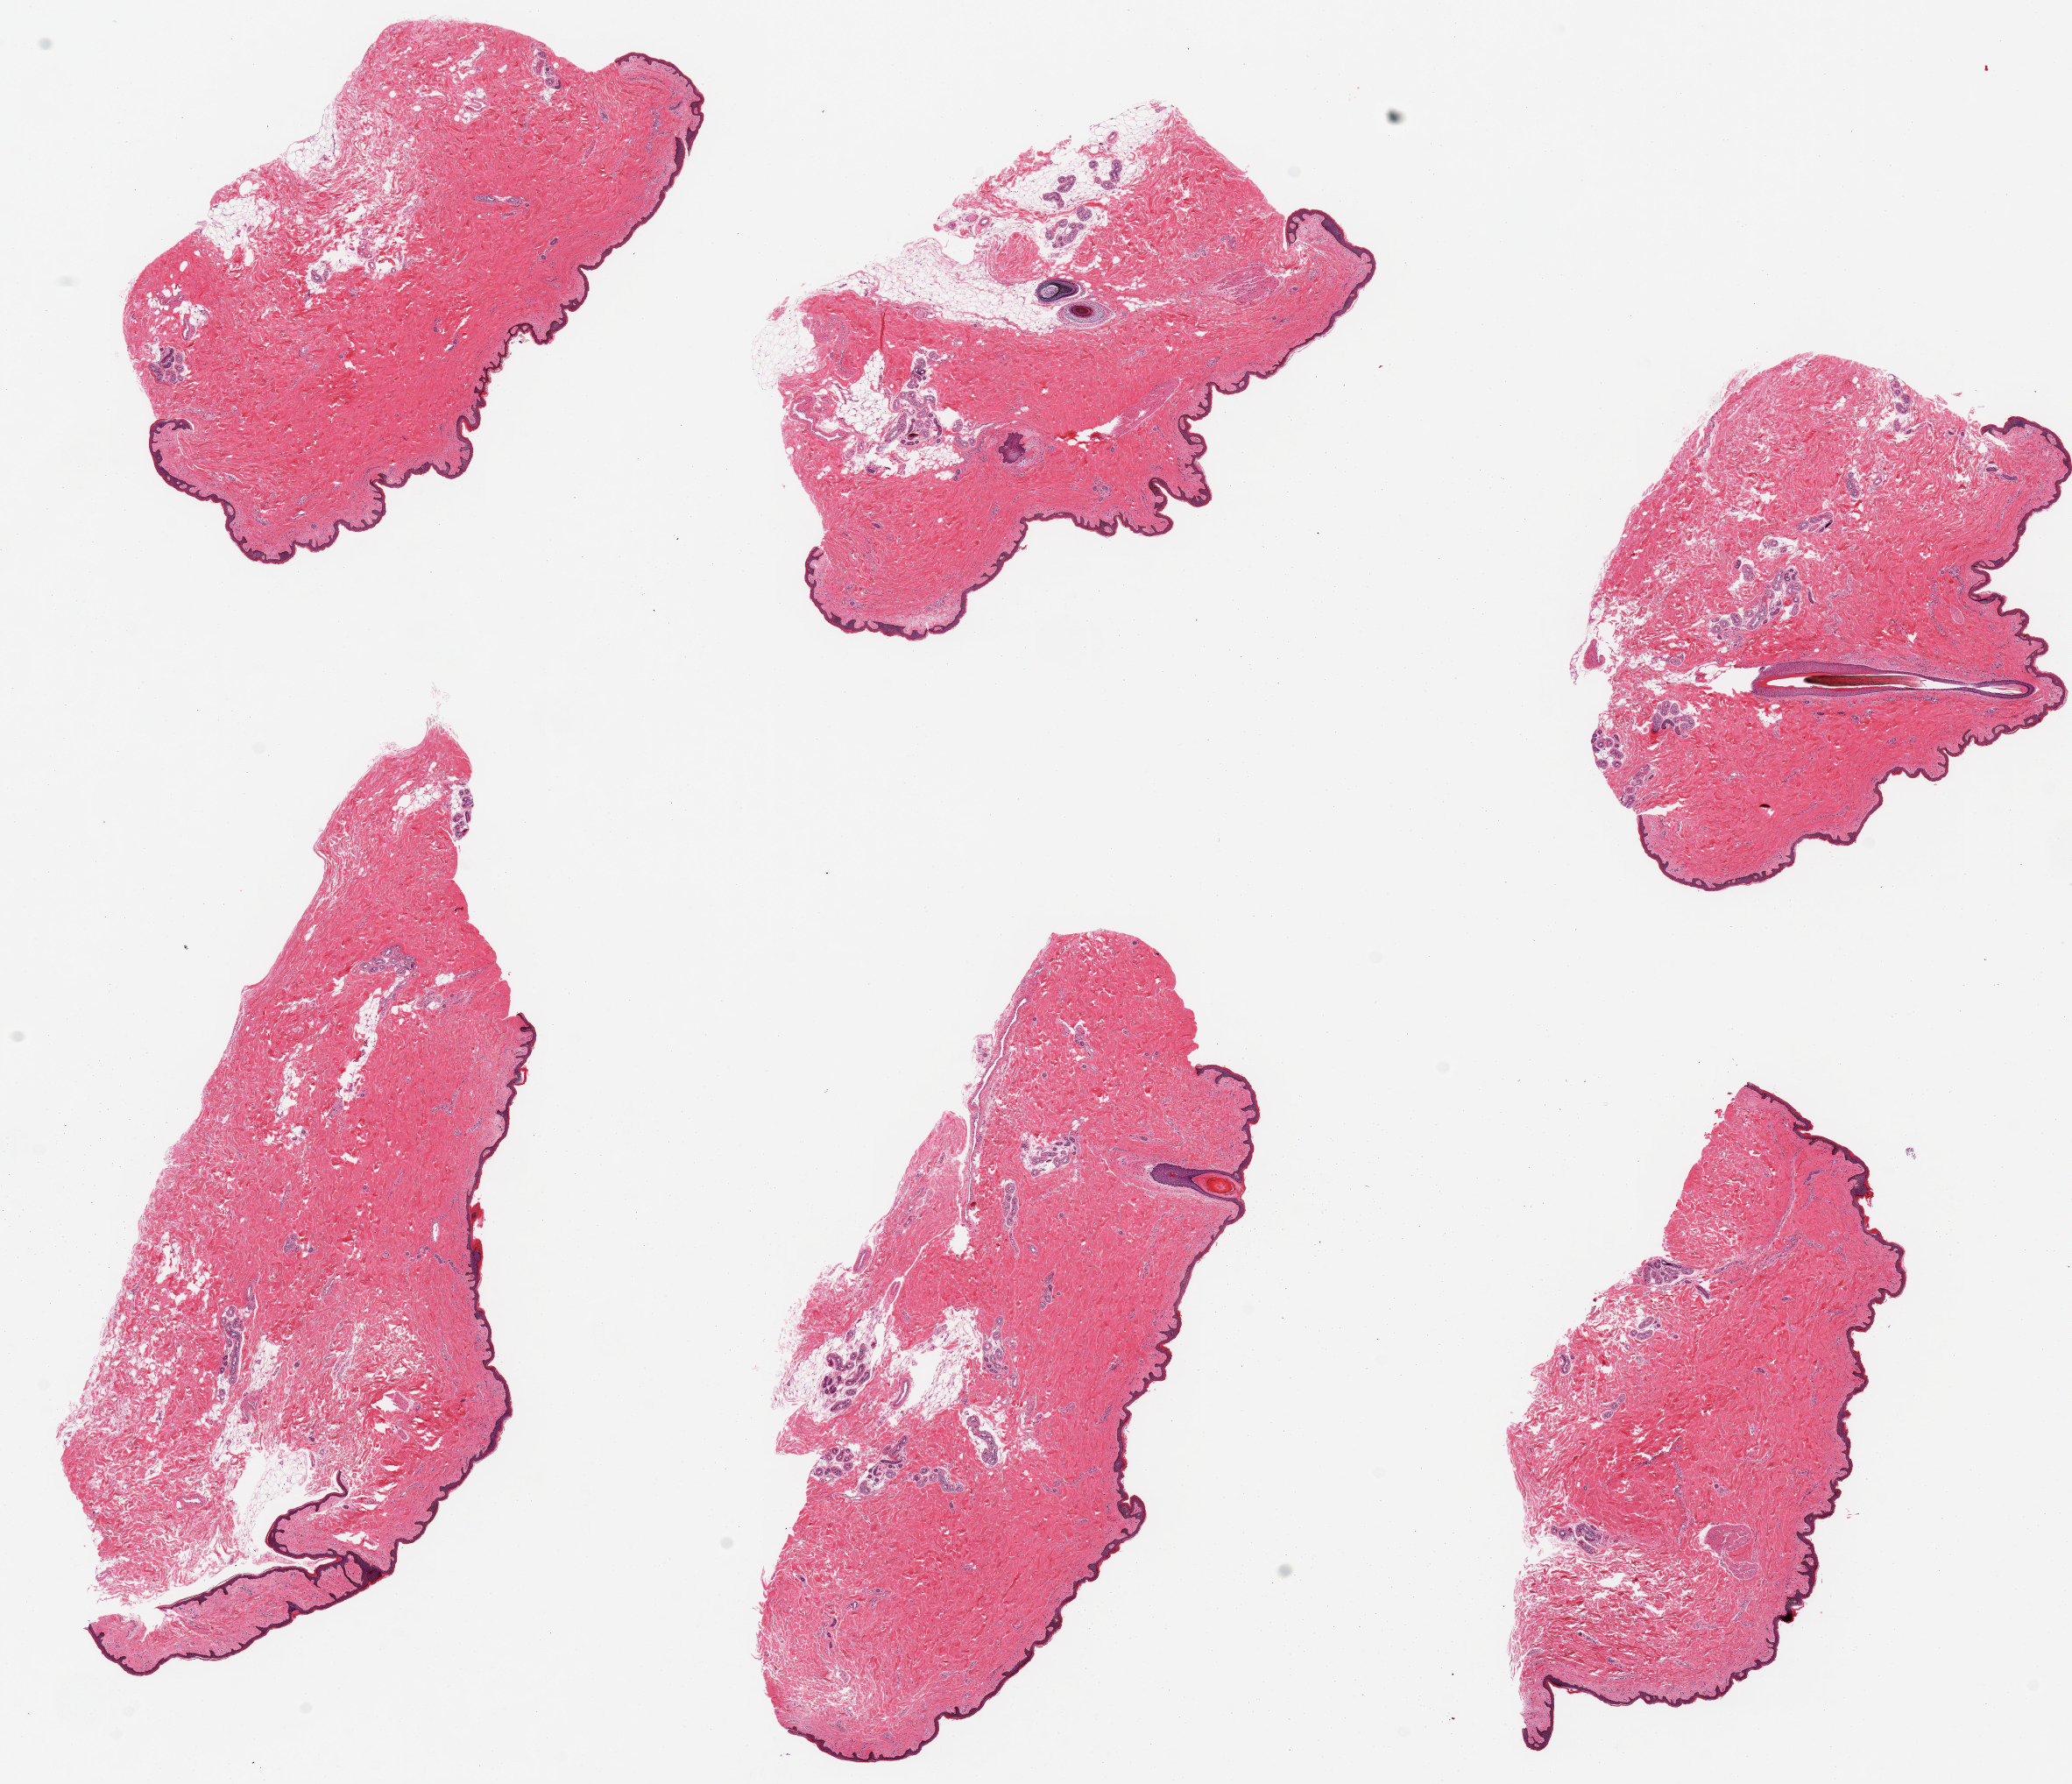
H&E whole-slide image, whole scanned area (about 18.7 x 16.1 mm, acquisition: 20x scan) shown as a low-resolution overview. PAXgene-fixed paraffin-embedded (PFPE) section. Section of skin of suprapubic region (target tissue). Donor tissue sample. Female donor.
Reviewer comment on this tissue sample: 6 pieces, up to 9x4mm.